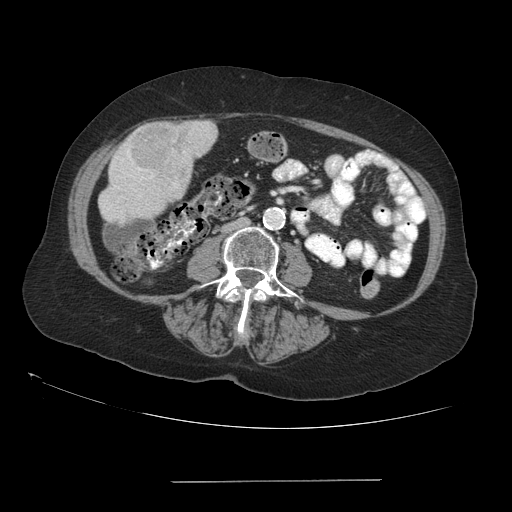
Contrast-enhanced abdominal CT (liver protocol), one axial slice. Position 20 of 89 along the scan axis. 140 kVp. Soft-tissue window (W 400 / L 40 HU). 2.5 mm slice thickness. 512 × 512 image matrix. Case-level facts recorded for this patient, not image findings: diagnosis: hepatocellular carcinoma (patient treated with transarterial chemoembolisation; whether this scan precedes or follows treatment is not stated here); TNM stage (as recorded): Stage-IVA; Child-Pugh class: A; tumour differentiation: poorly differentiated.
Outlined on this slice (semi-automatically segmented with operator editing):
- liver parenchyma outside the tumour (the mass and vessels are separate outlines, so this box may not span the whole liver): bounding box <98,120,216,224> (left, top, right, bottom; pixels)
- mass: <127,120,217,186>